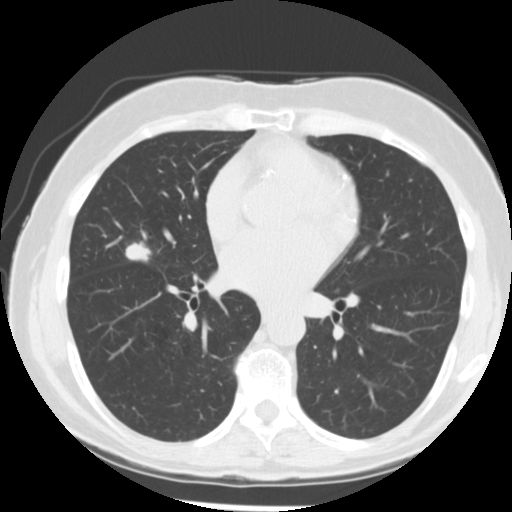
Axial slice from a low-dose chest CT screening exam, first (baseline) screen, lung window (W 1500 / L -600 HU), 2.5 mm slice thickness, standard (soft-tissue) reconstruction kernel (STANDARD), 512 × 512 image matrix. Female participant, aged 66 years at enrolment.
Expert reader's lesion annotation, box from (x=120, y=233) to (x=165, y=268) px. Screening reader's record for this exam (one nodule recorded; not confirmed to be the boxed lesion): non-calcified nodule or mass ≥4 mm, right middle lobe, 15 × 13 mm, poorly defined margins, soft tissue attenuation. Later outcome: lung cancer diagnosed 27 days after this screen — adenocarcinoma, NOS, right middle lobe, undifferentiated (G4), stage IIIA (AJCC 6th edition), 18 mm at pathology.